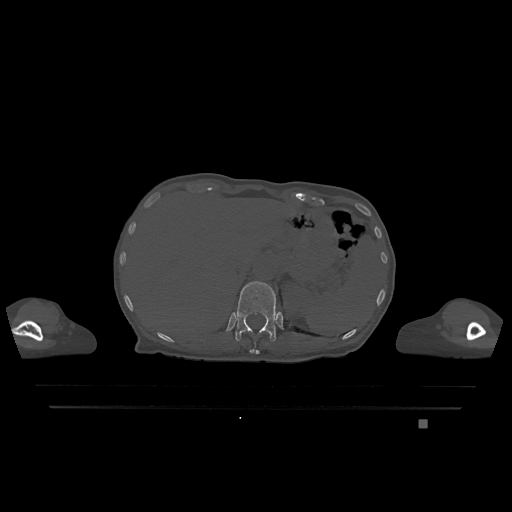
CT including the spine, one axial slice. Slice 546 of 1317 in the series (ordered by position). Bone window (W 1800 / L 400 HU). 512 × 512 image matrix. Patient: female, 74 years. Case-level facts recorded for this patient, not image findings: primary cancer: lung.
Outlined on this slice (semi-automatically segmented with operator editing):
- T11 vertebra: box from (x=250, y=343) to (x=260, y=354) px
- T12 vertebra: (x=235, y=281)–(x=276, y=342)